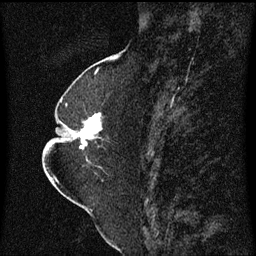
Breast MRI (dynamic contrast-enhanced), one sagittal slice; dynamic contrast-enhanced series, image 2 of 3 at this slice position (ordered by acquisition); 1.5 T; TE 4.2 ms, TR 8.4 ms; 256 × 256 image matrix, field of view 200 × 200 mm. Female patient, age 52 years. From the clinical record (not read from this slice): setting: breast cancer imaged before/during neoadjuvant chemotherapy; receptor status: HR-positive, HER2-negative.
Annotated regions visible in this slice (semi-automatically segmented with operator editing):
- analysis volume of interest (the breast-tissue region the enhancement analysis was run in; not a lesion): bounding box (x1, y1, x2, y2) in pixels: (64, 104, 105, 163)
- tumour enhancement mask (voxels above the 70 % enhancement threshold inside the analysis volume of interest): (78, 114, 101, 149)